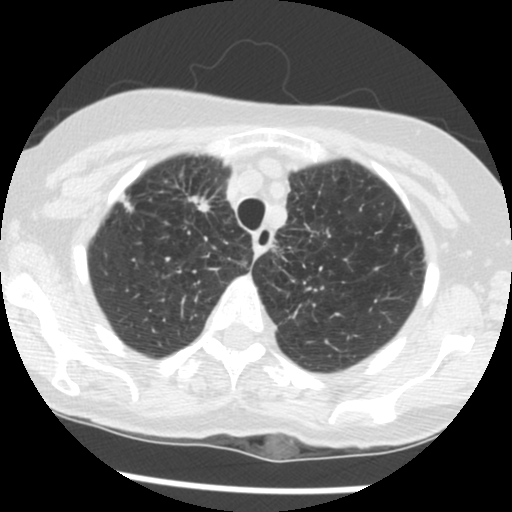
Low-dose screening chest CT, one axial slice; slice 102 of 124 in the series (ordered by position); 120 kVp; lung window (W 1500 / L -600 HU); 2.5 mm slice thickness; 512 × 512 image matrix, field of view 290 × 290 mm.
Annotated regions visible in this slice (expert manual segmentation):
- lesion 1 (tumor, upper lobe of right lung): bounding box <189,196,210,212> (left, top, right, bottom; pixels)